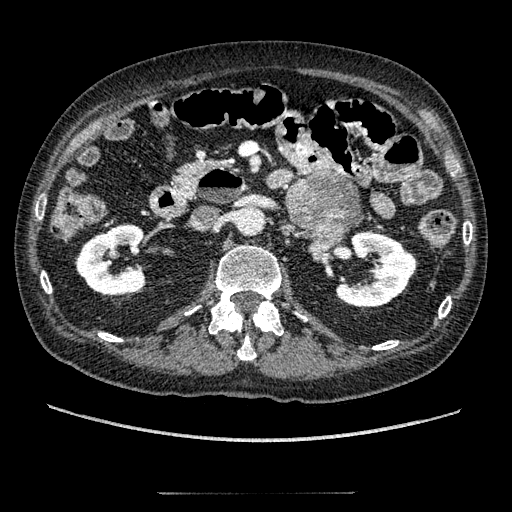
Contrast-enhanced abdominal CT, one axial slice. Slice 94 of 274 in the series (ordered by position). 120 kVp. Intravenous contrast given. Soft-tissue window (W 400 / L 40 HU). 1.25 mm slice thickness. 512 × 512 image matrix, field of view 381 × 381 mm. Male patient, age 69 years. Case-level facts recorded for this patient, not image findings: diagnosis: adrenocortical carcinoma; tumour side: left adrenal; tumour size at pathology: 6.1 cm; Ki-67 index: 10 %.
Structures marked on this image (semi-automatic segmentation, software-assisted and operator-edited):
- mass: bounding box [x1, y1, x2, y2] px = [287, 172, 360, 248]